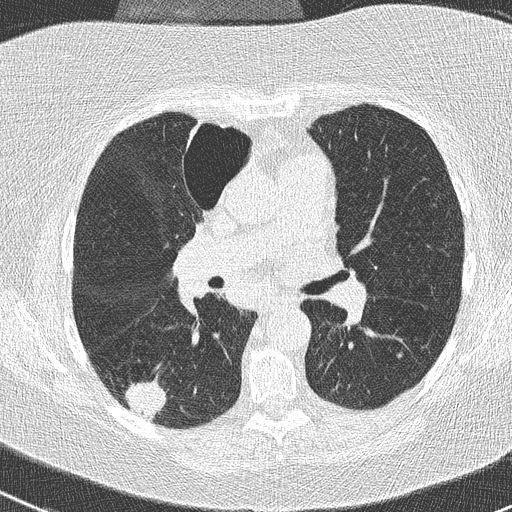
Low-dose screening chest CT, one axial slice. Slice 148 of 261 in the series (ordered by position). Reconstruction kernel B50f. 120 kVp. Lung window (W 1500 / L -600 HU). 2 mm slice thickness. 512 × 512 image matrix, field of view 310 × 310 mm.
Outlined on this slice (outlined manually by an expert reader):
- lesion 1 (tumor, lower lobe of right lung): bounding box [x1, y1, x2, y2] px = [125, 381, 167, 420]